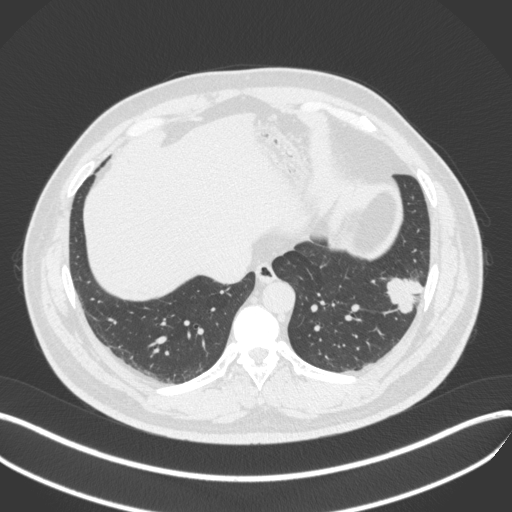
Chest CT, one axial slice. Reconstruction kernel B31f. Lung window (W 1500 / L -600 HU). 1 mm slice thickness. 512 × 512 image matrix. Male patient, age 39 years. Case-level facts recorded for this patient, not image findings: clinical TNM (as recorded): T2a N0 M0.
Annotated regions visible in this slice (rectangle marked by the reading radiologist):
- lung tumour (recorded histology: adenocarcinoma): bounding box [x1, y1, x2, y2] px = [379, 264, 432, 315]